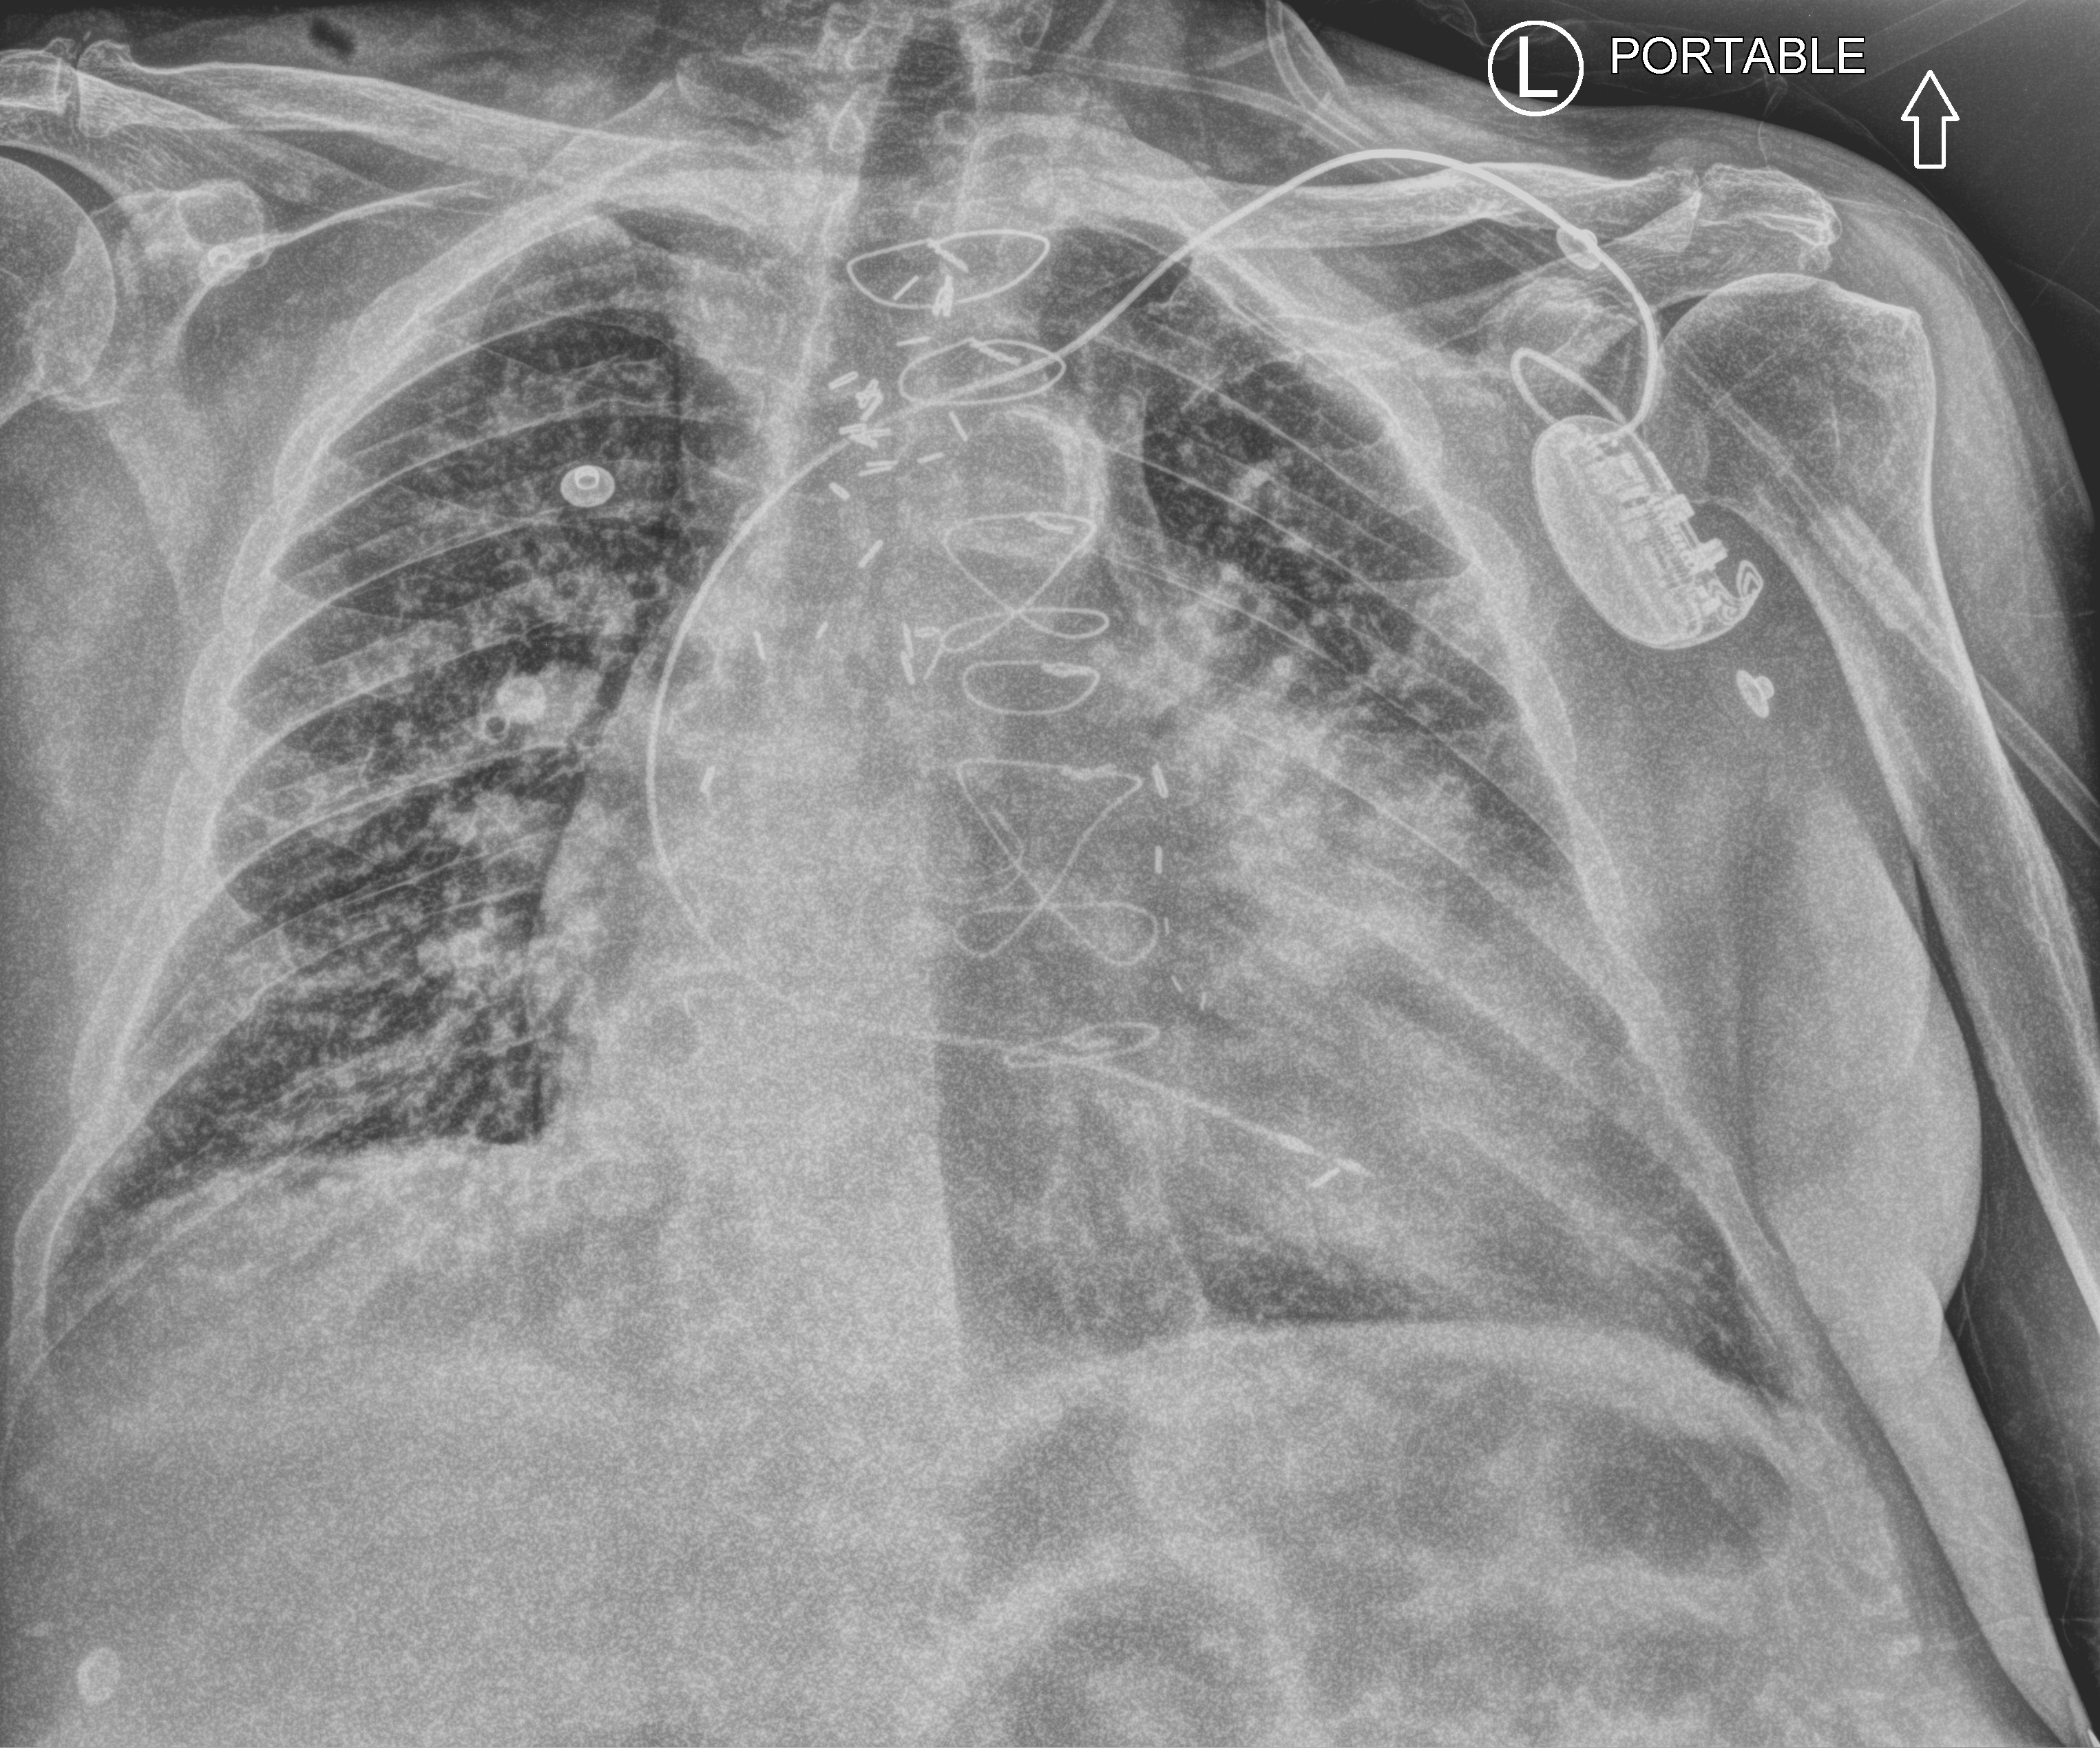
Bedside chest radiograph (computed radiography); anteroposterior (AP) projection. Patient hospitalised with COVID-19; male, aged 75–90 years.
Hospital-stay facts (about this admission, not read from this image; timing relative to this image not recorded): admitted to intensive care during this hospital stay: yes.